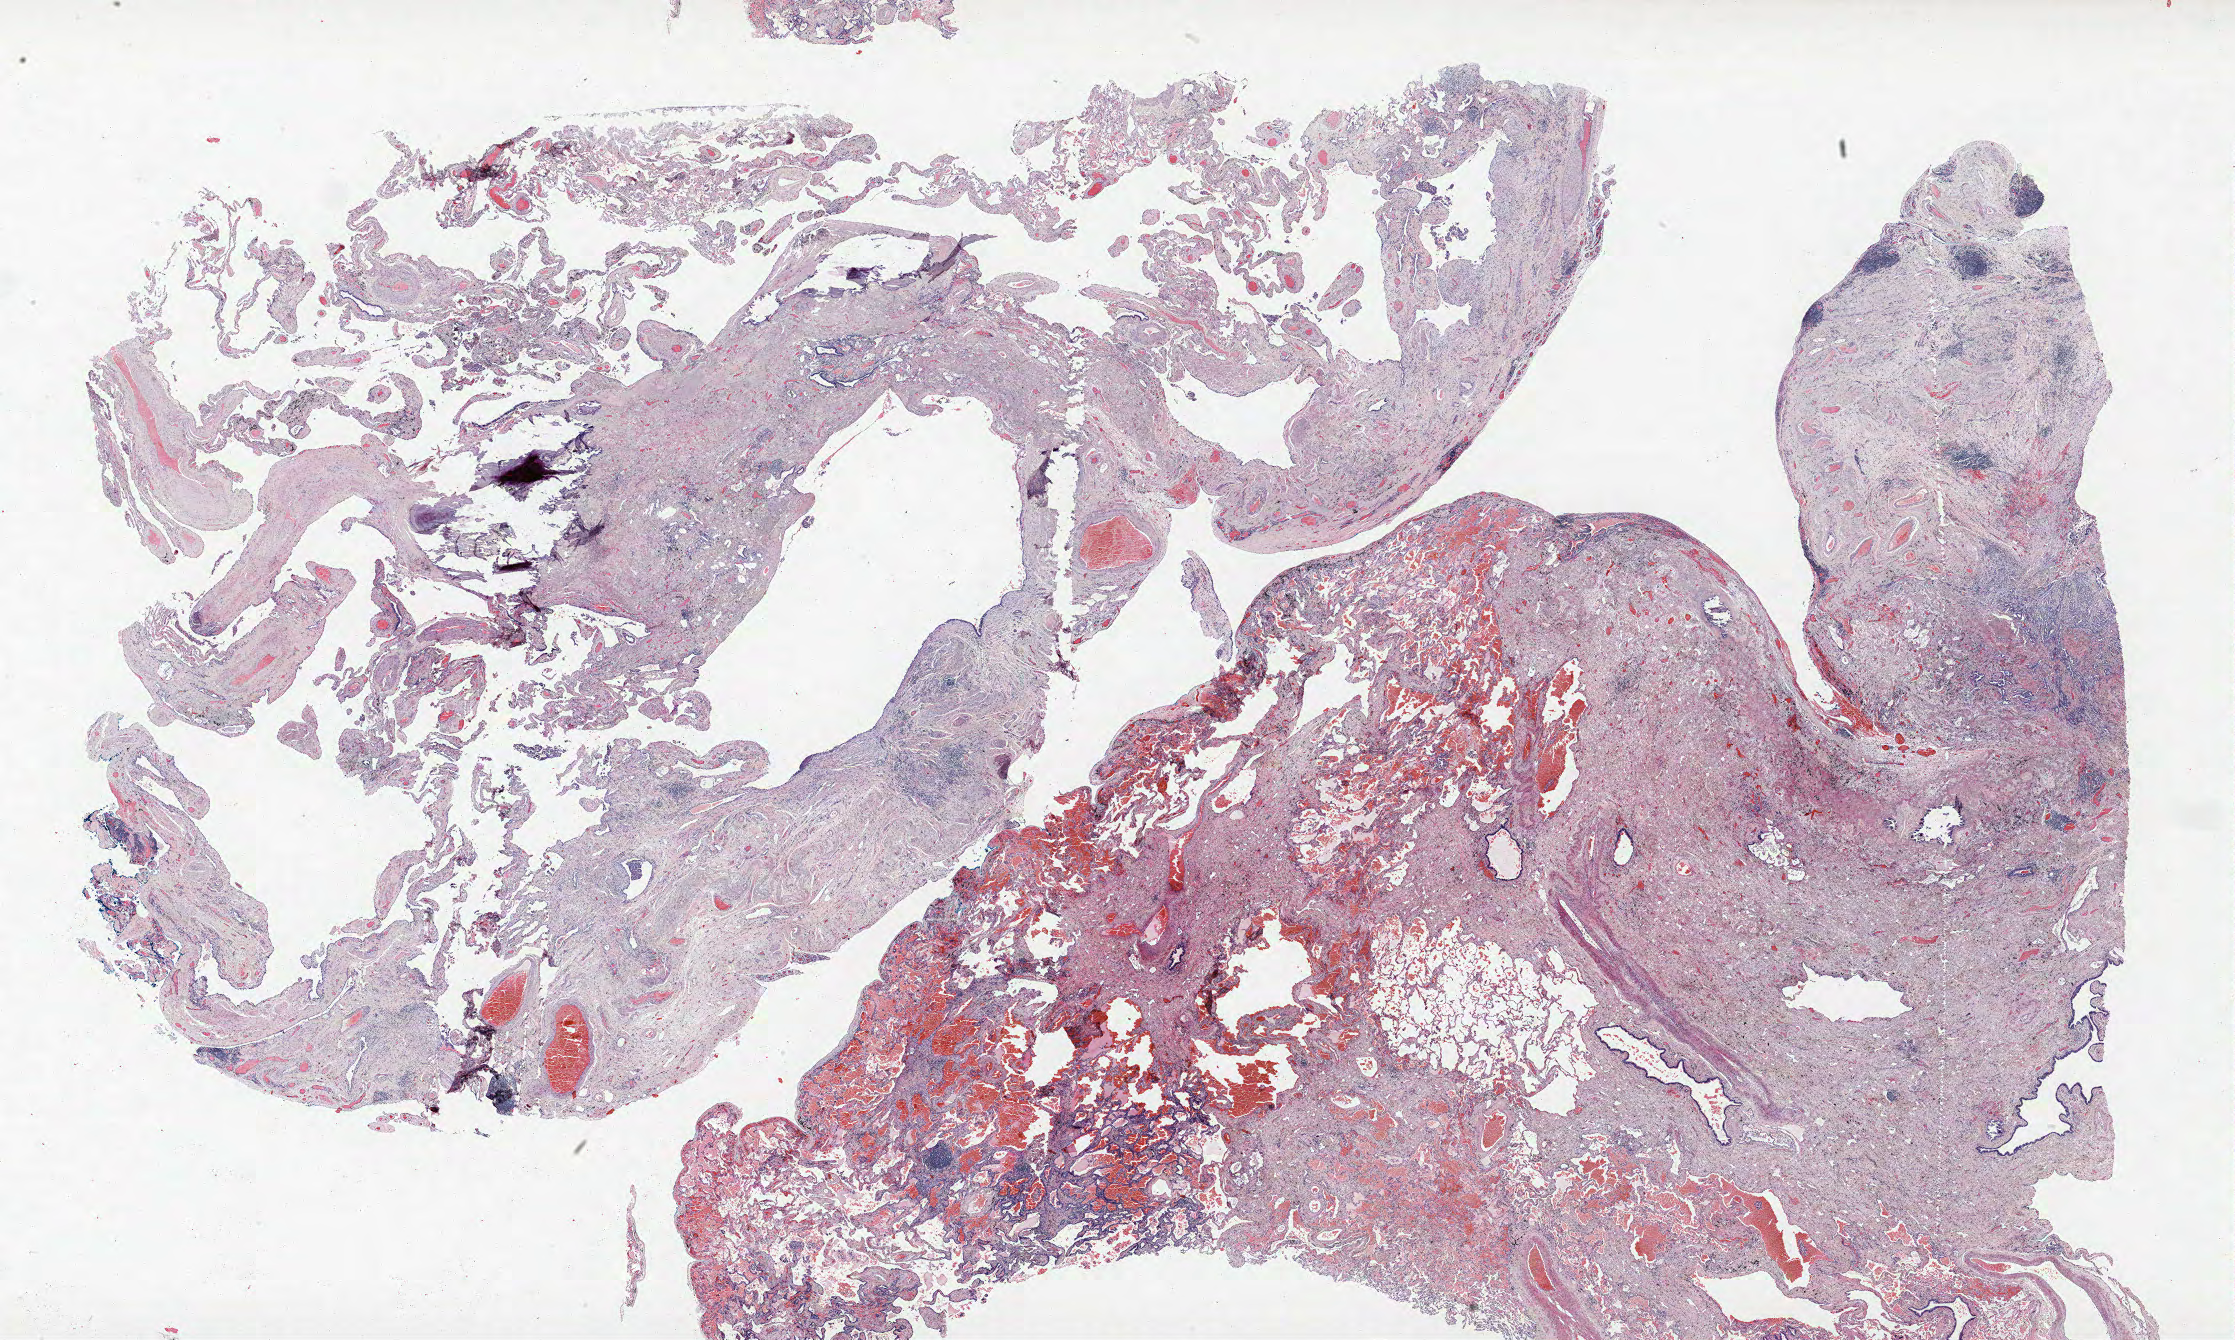
Whole-slide histology image, H&E-stained — shown as a low-resolution overview of the whole scanned area (about 35.8 x 21.4 mm, slide scanned at 40x), formalin-fixed paraffin-embedded (FFPE) section, lung tissue. Male patient, aged 67 at enrolment. Former smoker at enrolment. Grade: moderately differentiated (G2).
Participant's lung-cancer diagnosis: Adenocarcinoma, NOS. Primary tumour location (clinical record): left upper lobe. Stage (AJCC 6th edition): IB. Tumour size (pathology): 40 mm.